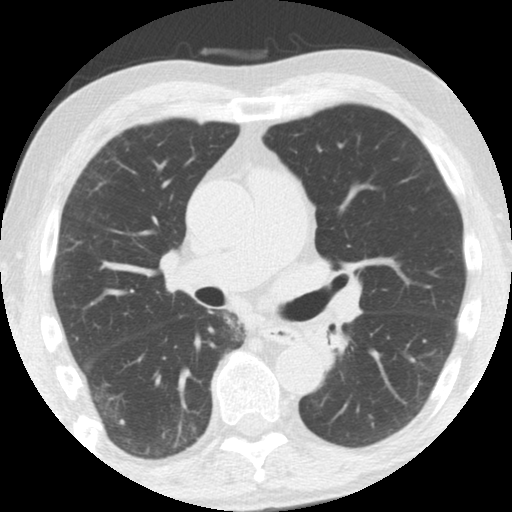
Axial slice from a low-dose chest CT screening exam, third annual screen, lung window (W 1500 / L -600 HU), standard (soft-tissue) reconstruction kernel (STANDARD), 120 kVp, 512 × 512 image matrix, field of view 308 × 308 mm. Male participant, aged 61 years at enrolment. Former smoker at enrolment.
Expert reader's lesion annotation, bounding box <294,316,345,362> (left, top, right, bottom; pixels). Screening reader's record for this exam: no non-calcified nodule ≥4 mm recorded. Official screen result: negative screen, minor abnormalities not suspicious for lung cancer. Later outcome: lung cancer diagnosed 363 days after this screen — squamous cell carcinoma, NOS, left upper lobe, left lower lobe, well differentiated (G1), stage IIB (AJCC 6th edition), 100 mm at pathology.